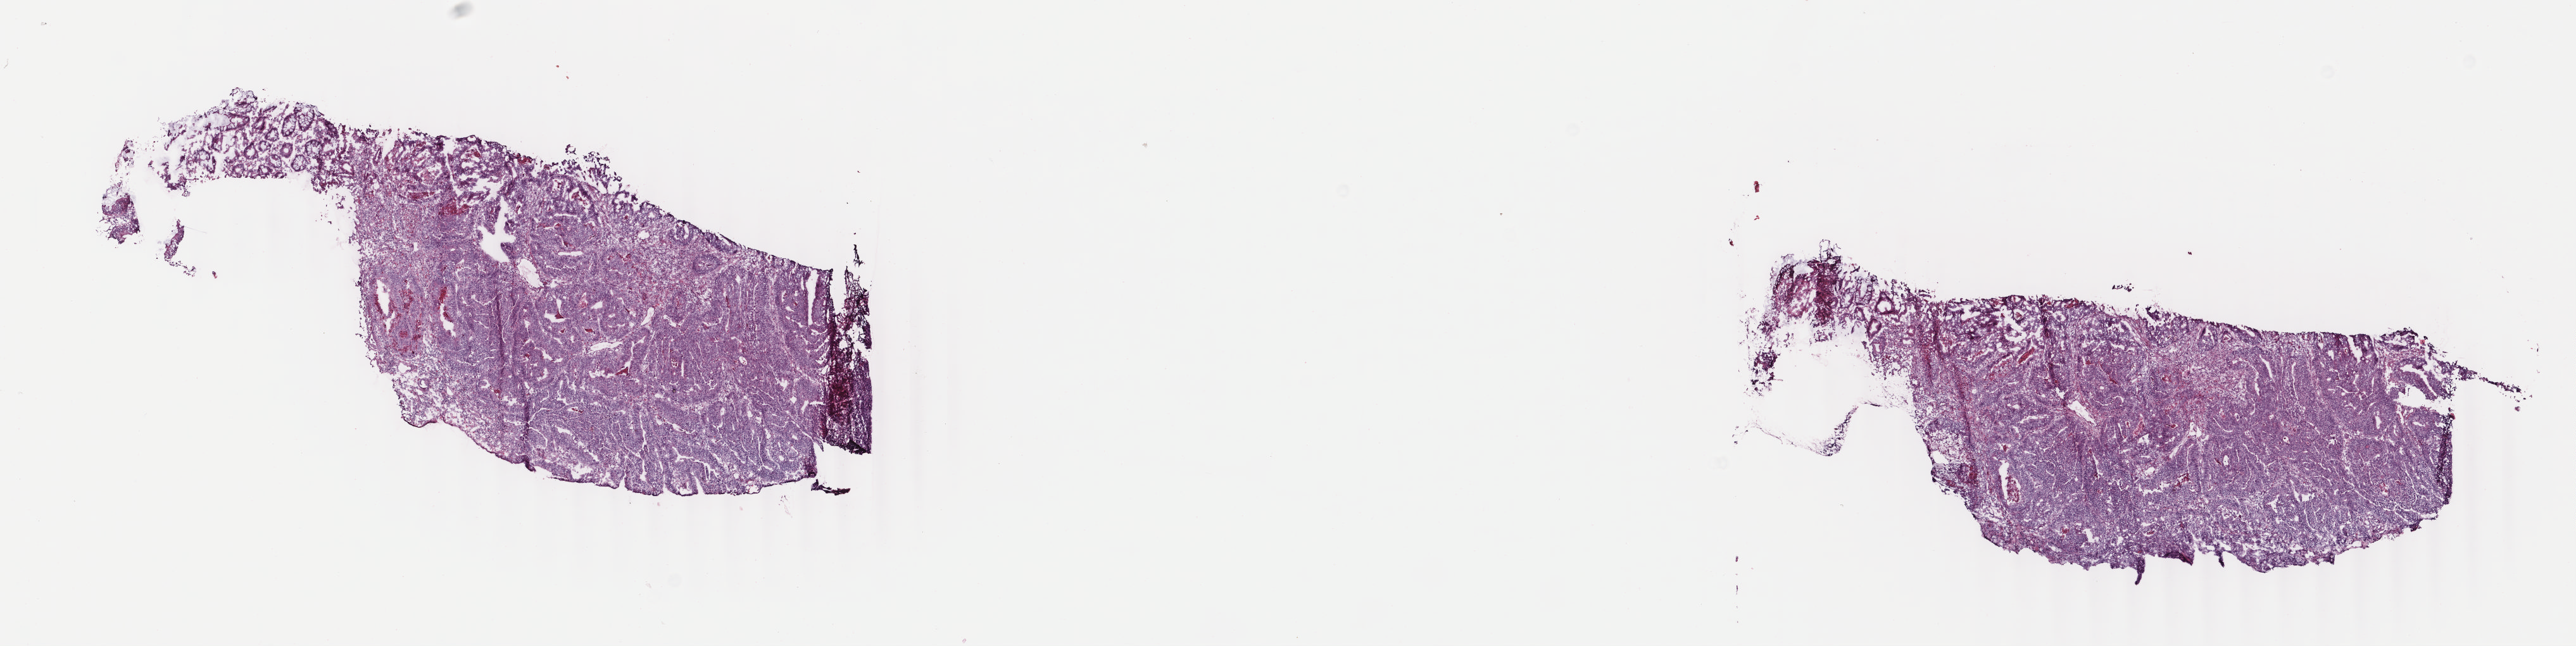
Digitized H&E tissue section (whole slide), shown as a low-resolution overview of the whole scanned area (about 16.2 x 4.1 mm, from a 40x scan); frozen section; colon, primary tumour sample. Female patient; age at initial diagnosis 65 years. Slide review estimates, as recorded: tumour cells 76%, tumour nuclei 82%, normal cells 7%, stromal cells 10%, necrosis 7%. Inflammatory infiltration, as recorded: lymphocyte infiltration 6%, monocyte infiltration 2%, neutrophil infiltration 2%.
- AJCC pathologic stage: I
- diagnosis: Adenocarcinoma, NOS
- lymph nodes positive (case pathology): 0 of 34 examined